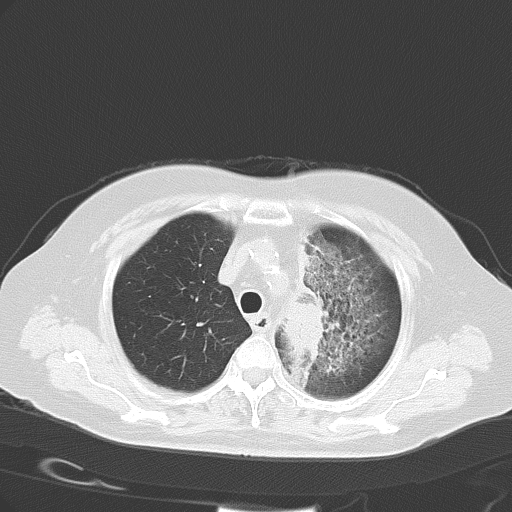
Chest CT, one axial slice. Position 43 of 54 along the scan axis. Reconstruction kernel B70f. 120 kVp. Lung window (W 1500 / L -600 HU). 5 mm slice thickness. 512 × 512 image matrix. Patient: female, 65 years. From the clinical record (not read from this slice): clinical TNM (as recorded): T2b N1 M0.
Structures marked on this image (rectangle marked by the reading radiologist):
- lung tumour (recorded histology: adenocarcinoma): bounding box (x1, y1, x2, y2) in pixels: (286, 300, 328, 360)